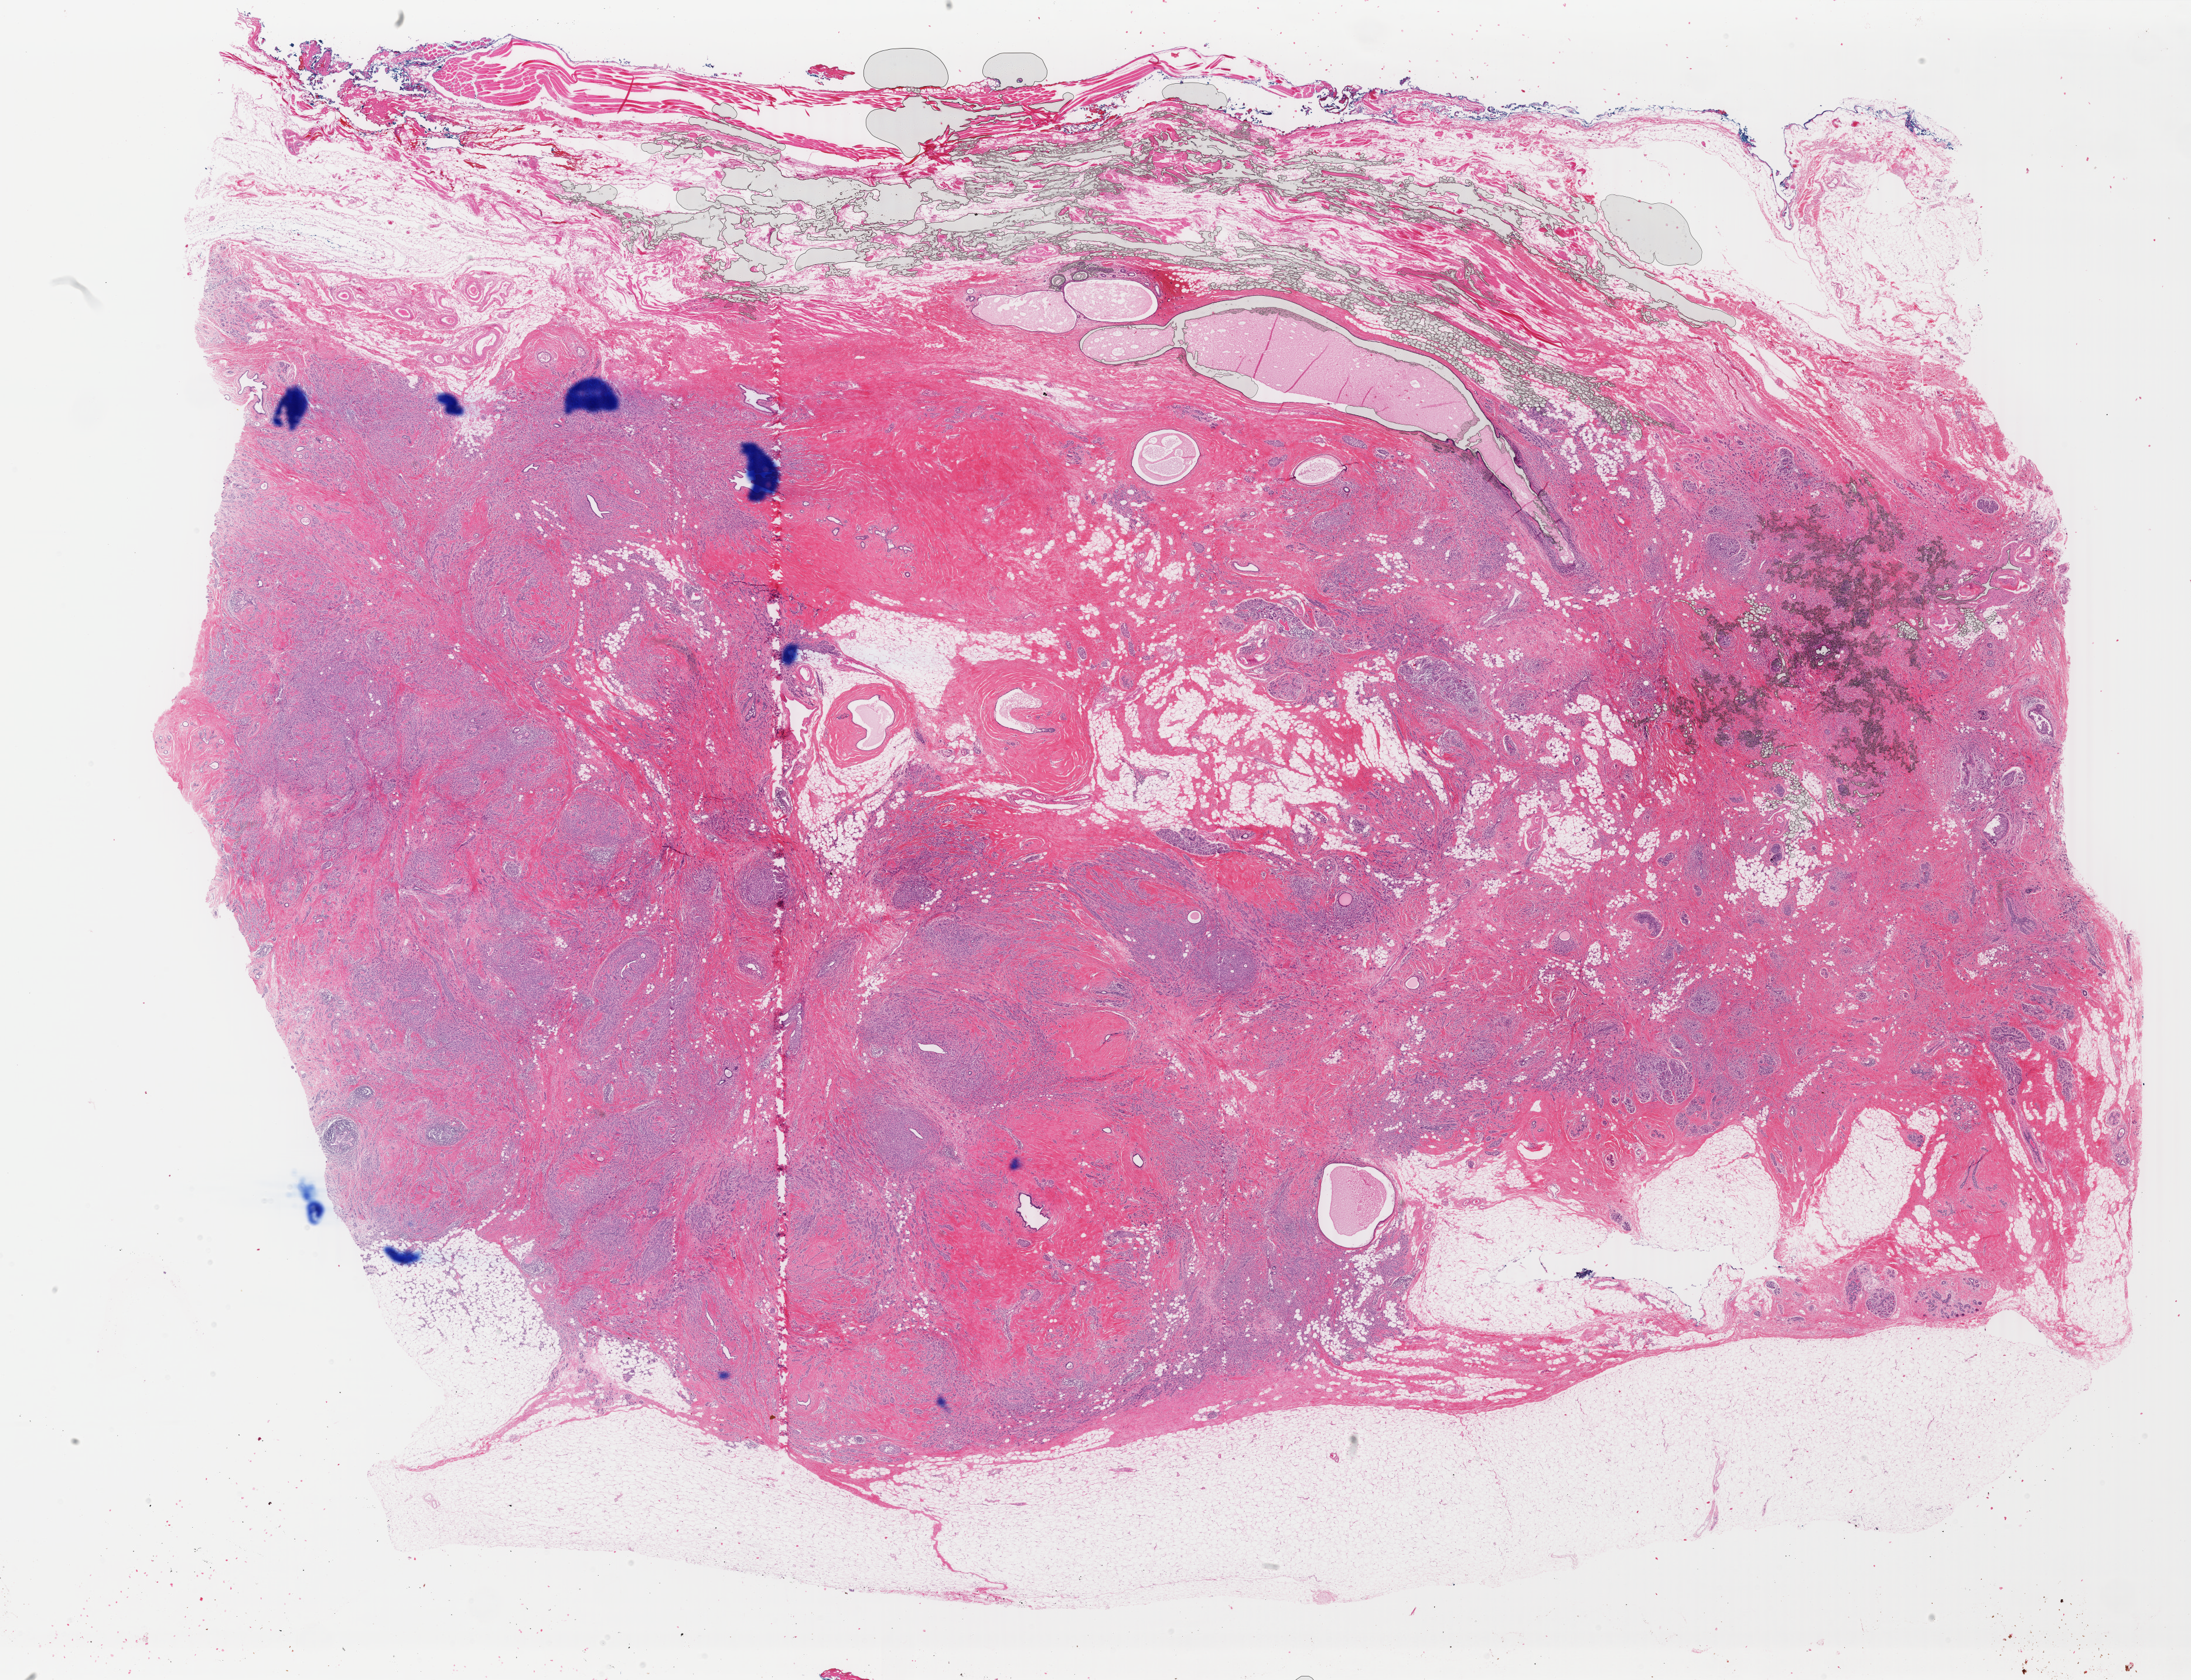
Hematoxylin and eosin (H&E) stained whole-slide image — low-resolution overview of the scanned area, about 29.7 x 22.8 mm (acquisition: 40x scan), FFPE section, breast, primary tumour sample. Female patient; age at initial diagnosis 42 years.
* pathologic diagnosis: Infiltrating duct and lobular carcinoma
* AJCC pathologic stage: IIIA